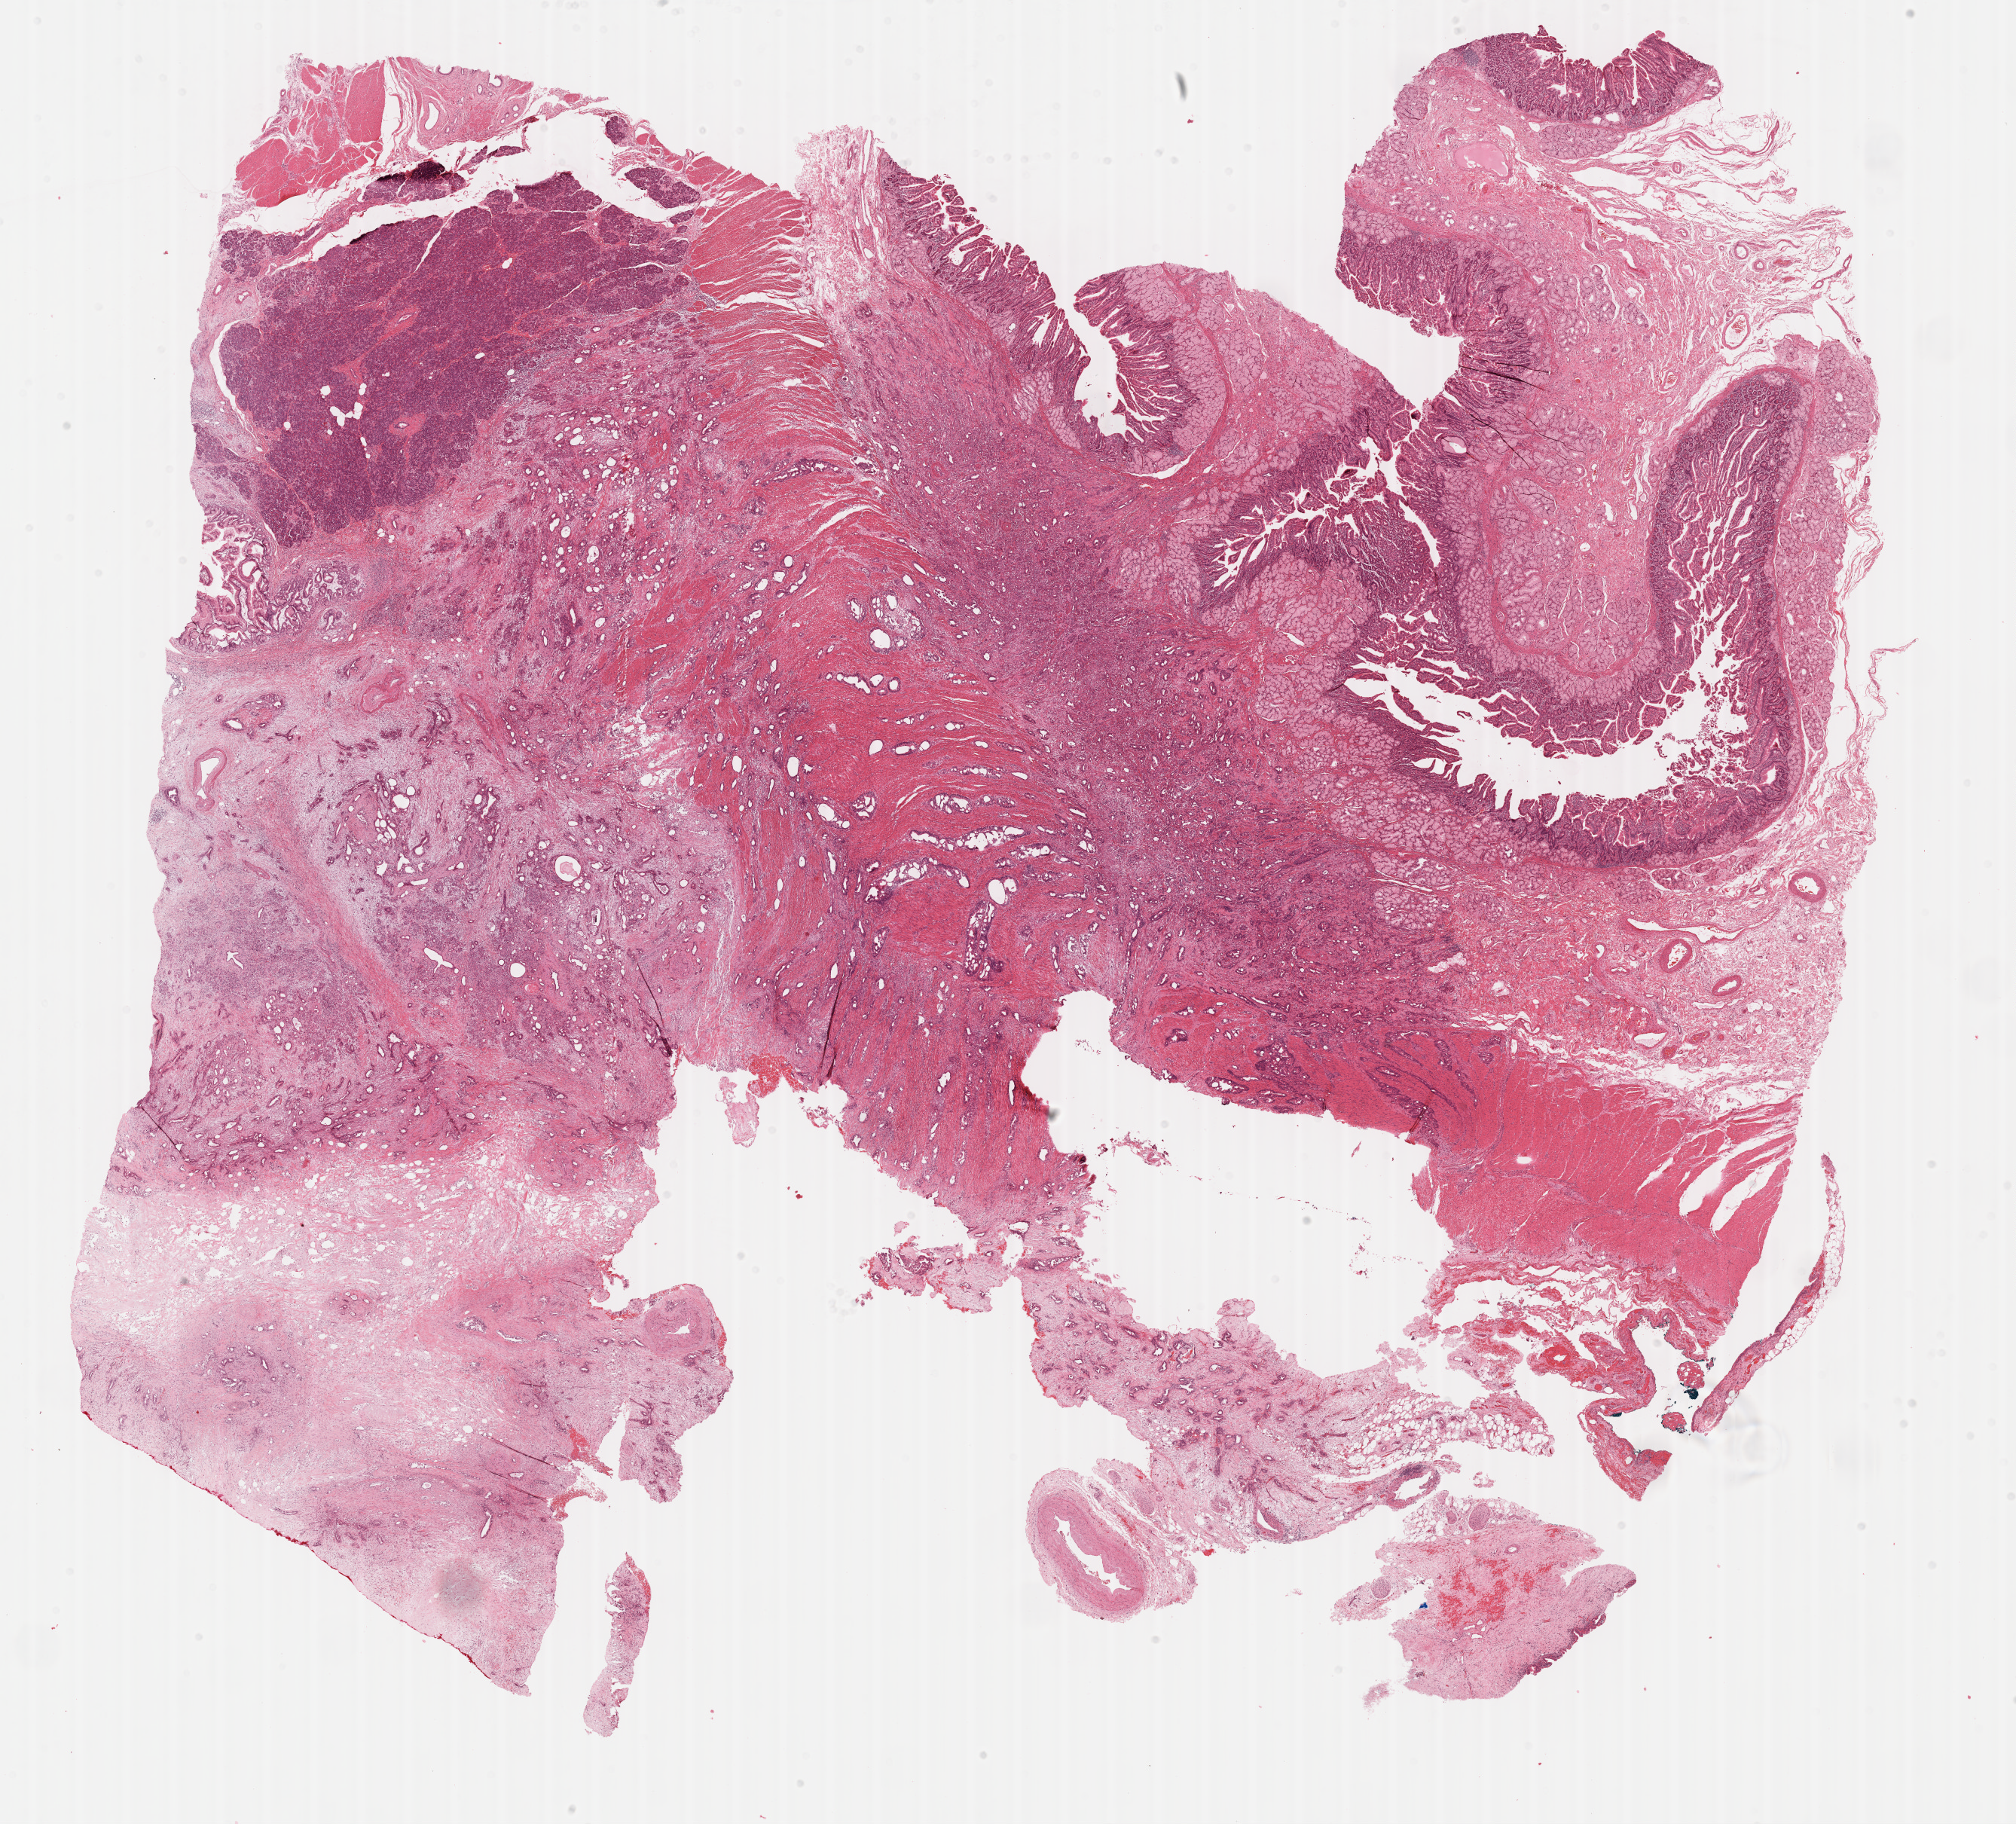
Hematoxylin and eosin (H&E) stained whole-slide image, shown as a low-resolution overview of the whole scanned area (about 21.6 x 19.6 mm, from a 40x scan), formalin-fixed paraffin-embedded (FFPE) diagnostic section, sample: primary tumour, pancreas. Patient: male, age at initial diagnosis 83 years. Histologic grade: G3 (poorly differentiated).
Lymph nodes positive (case pathology): 2 of 18 examined. Histologic diagnosis: Infiltrating duct carcinoma, NOS. AJCC pathologic stage: IIA (6th edition).